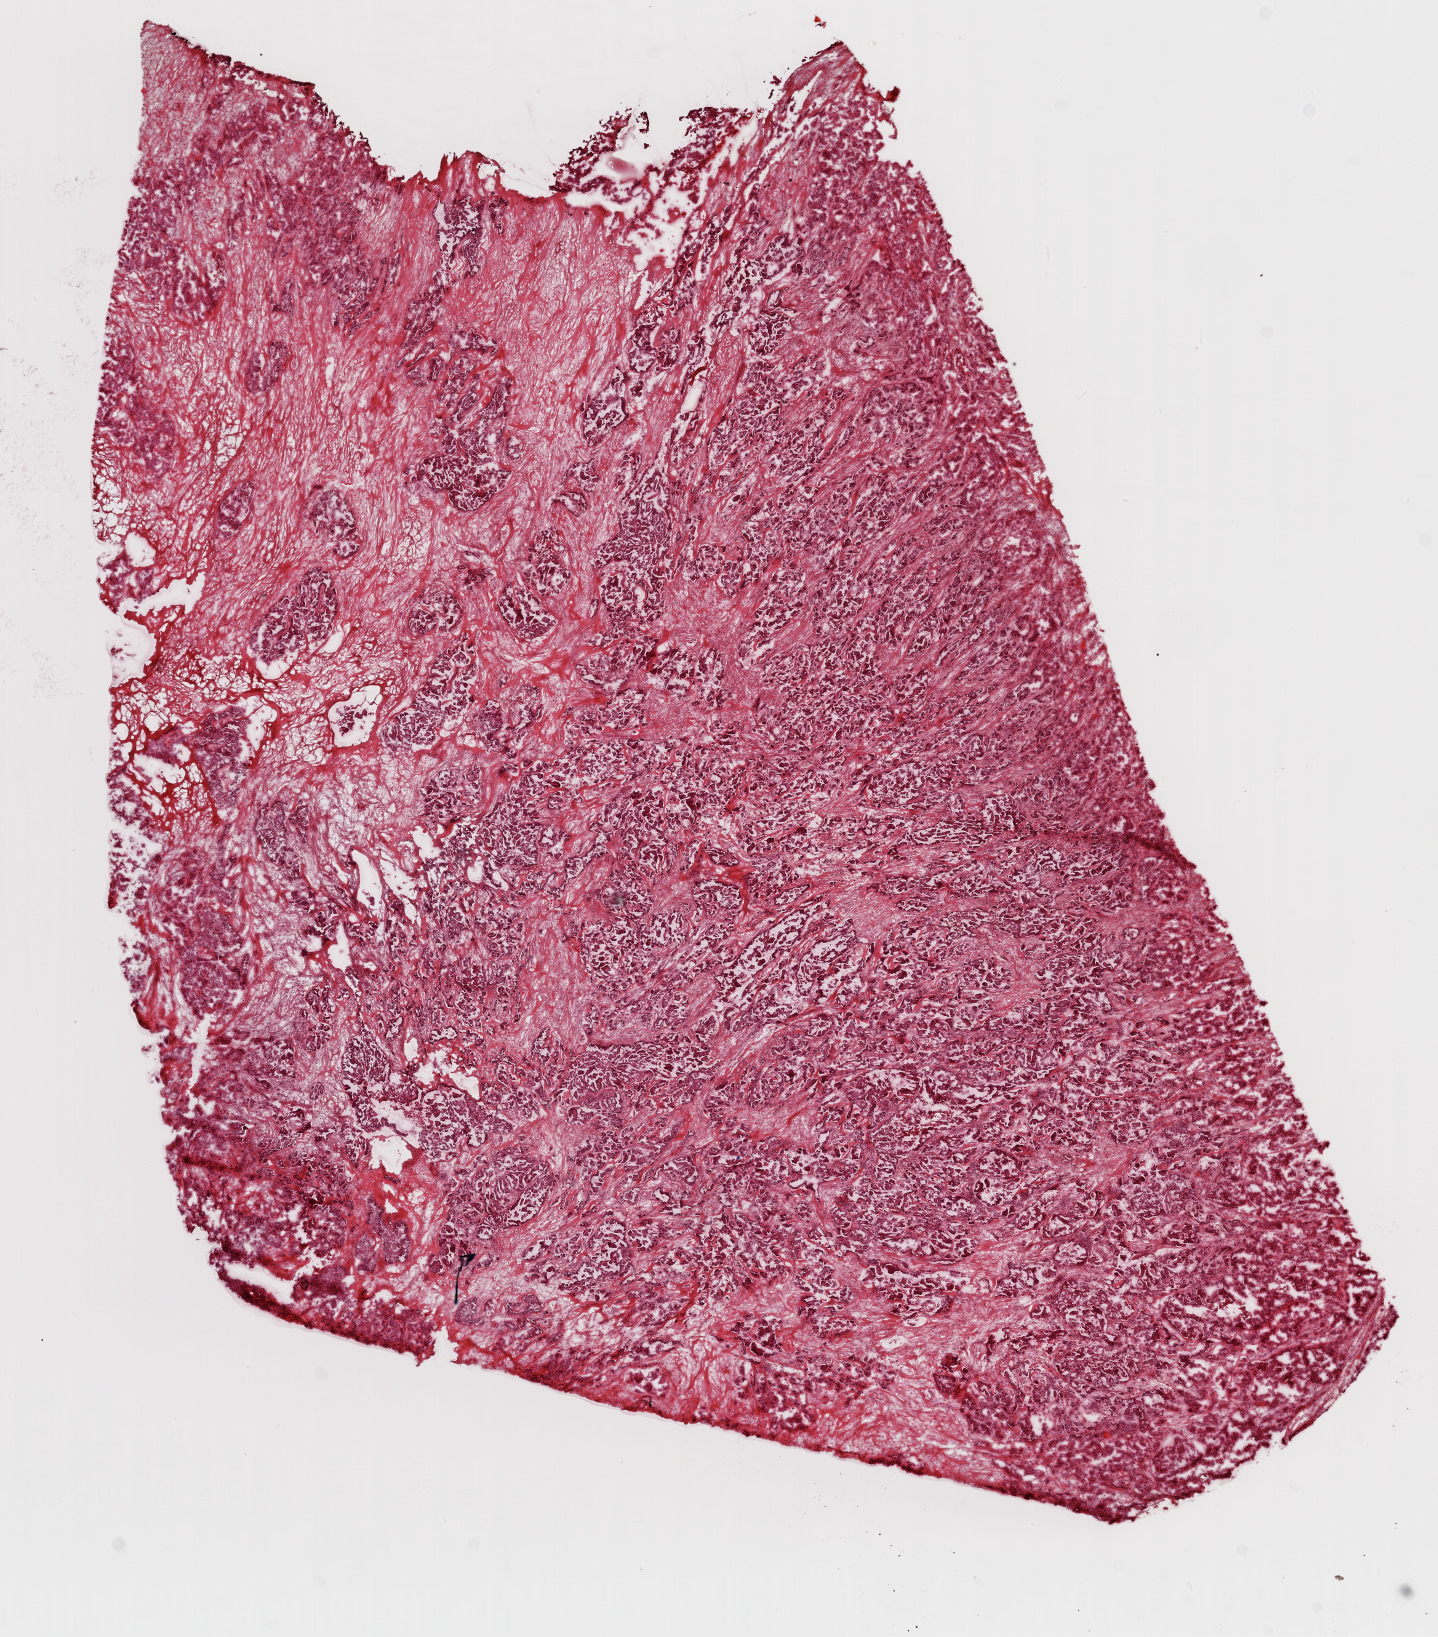
Hematoxylin and eosin (H&E) stained whole-slide image, whole scanned area (about 11.6 x 13.2 mm, acquisition: 20x scan) shown as a low-resolution overview; frozen section from the top of the tissue portion; ovary, primary tumour sample. Female, age 36 years at initial diagnosis. Histologic grade: G3 (poorly differentiated). Pathologist review of this section (percent, as recorded): tumour nuclei 90%, necrosis 1%.
- FIGO stage: IIIC
- pathologic diagnosis: Serous cystadenocarcinoma, NOS
- laterality: bilateral